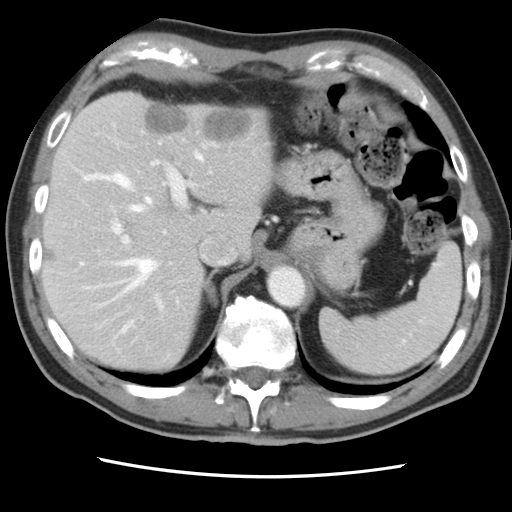
Contrast-enhanced abdominal CT, one axial slice. 120 kVp. Intravenous contrast given. Soft-tissue window (W 400 / L 40 HU). 5 mm slice thickness. 512 × 512 image matrix. Male patient, age 69 years. From the clinical record (not read from this slice): diagnosis: colorectal cancer liver metastases, imaged before liver resection; multiple liver metastases: yes.
Outlined on this slice (expert manual segmentation):
- hepatic veins: bounding box <80,153,211,331> (left, top, right, bottom; pixels)
- liver: <43,92,269,371>
- planned liver remnant (the part of the liver to remain after resection): <43,143,210,371>
- portal vein (with intrahepatic branches): <111,160,195,310>
- liver metastasis: <145,105,189,134>
- liver metastasis: <204,110,251,141>